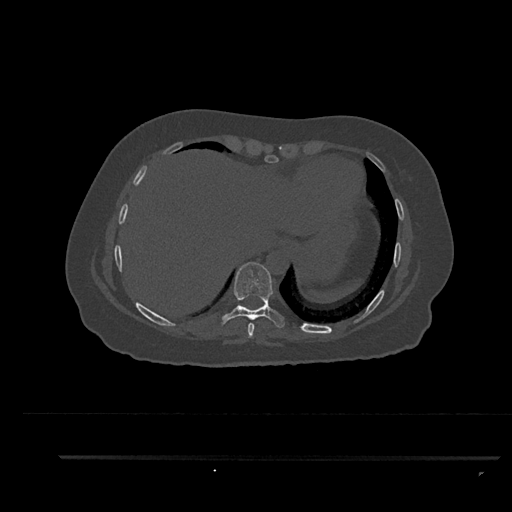
CT including the spine, one axial slice. Slice 418 of 797 in the series (ordered by position). Reconstruction kernel Br40s/3. Bone window (W 1800 / L 400 HU). 0.5 mm slice thickness. 512 × 512 image matrix, field of view 408 × 408 mm. Female patient, age 44 years. From the clinical record (not read from this slice): primary cancer: renal; vertebrae with lytic lesions (as recorded): L1.
Structures marked on this image (semi-automatic segmentation, software-assisted and operator-edited):
- T8 vertebra: box from (x=247, y=323) to (x=255, y=338) px
- T9 vertebra: (x=220, y=262)–(x=285, y=328)